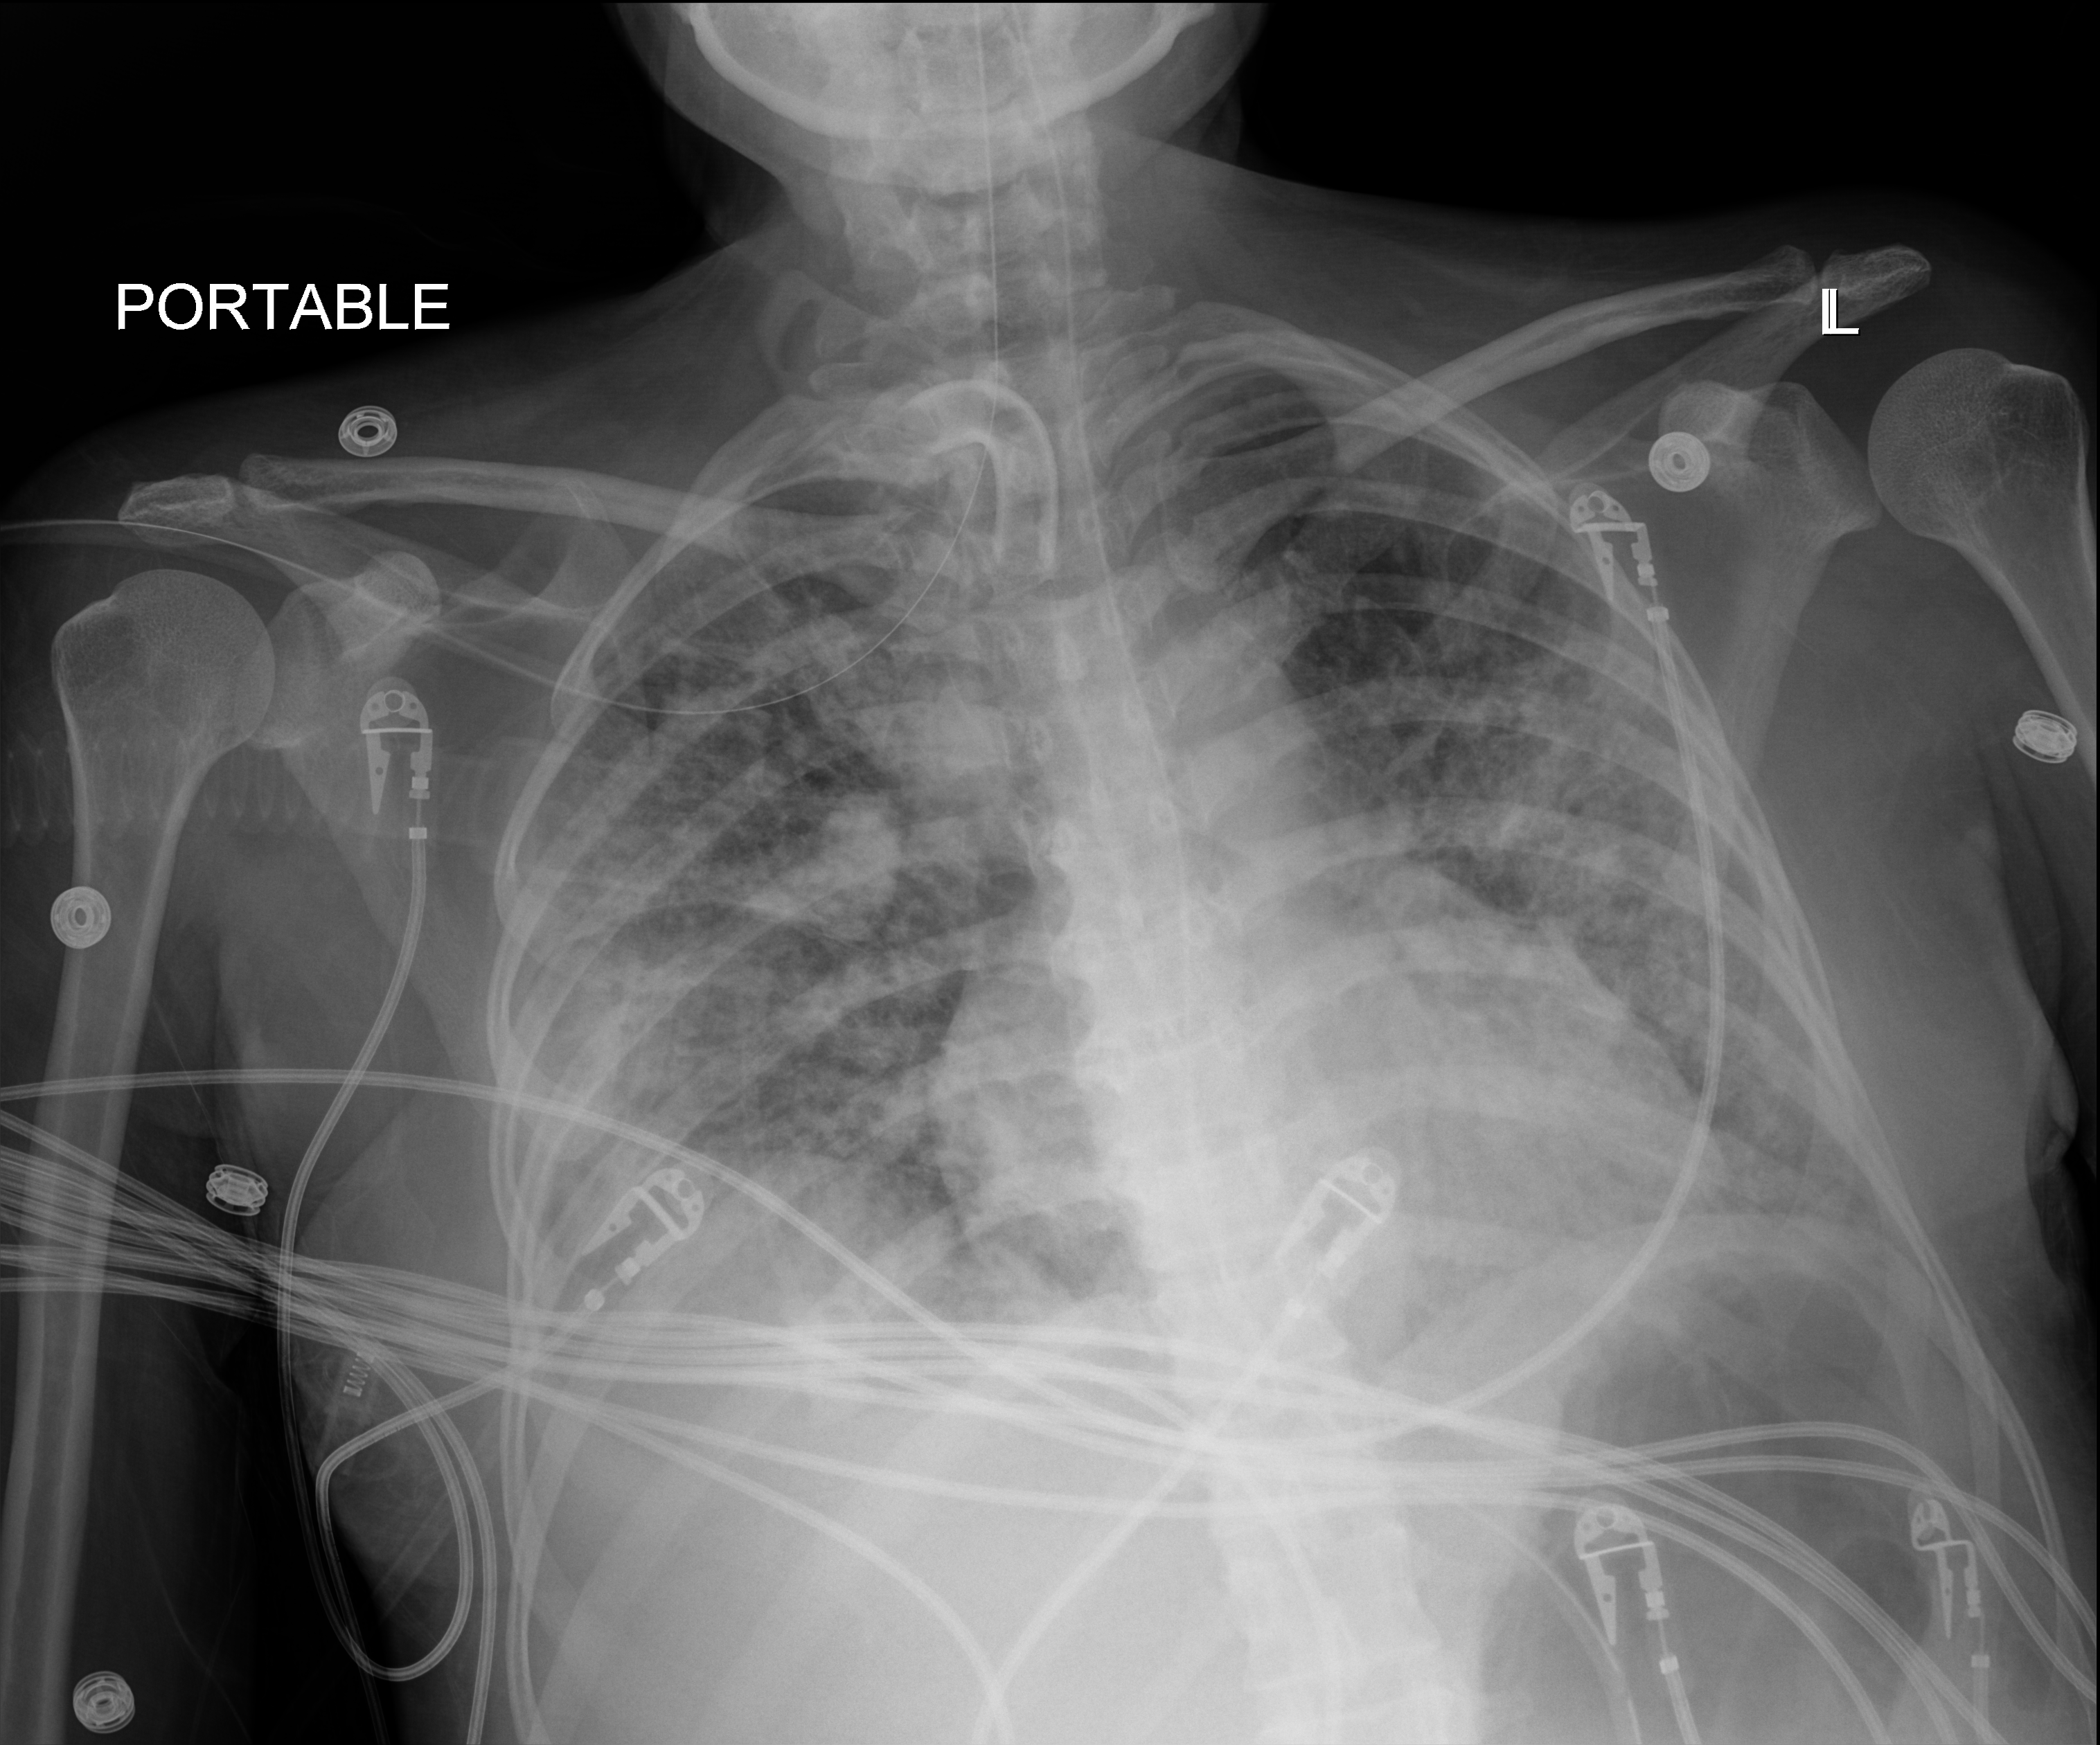
Portable chest radiograph; anteroposterior (AP) projection. Female patient hospitalised with COVID-19, age 18–59 years.
Hospital-stay facts (about this admission, not read from this image; timing relative to this image not recorded): COPD (admission record): no; chronic kidney disease (admission record): no.